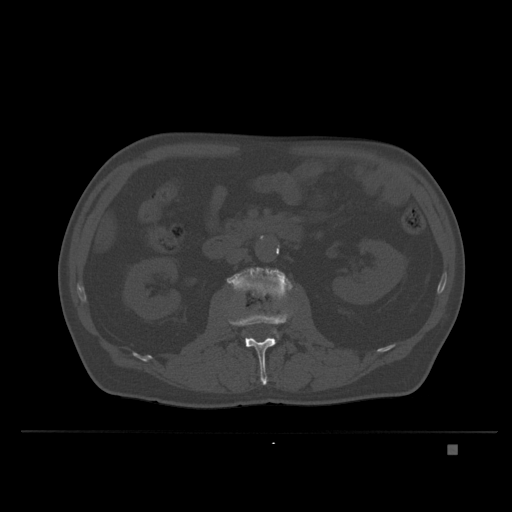
CT including the spine, one axial slice. Position 111 of 435 along the scan axis. Bone window (W 1800 / L 400 HU). 1.5 mm slice thickness. 512 × 512 image matrix, field of view 434 × 434 mm. Patient: male, 73 years. Case-level facts recorded for this patient, not image findings: primary cancer: skin.
Structures marked on this image (semi-automatically segmented with operator editing):
- L2 vertebra: bounding box [x1, y1, x2, y2] px = [228, 305, 293, 385]
- L3 vertebra: [226, 267, 292, 298]